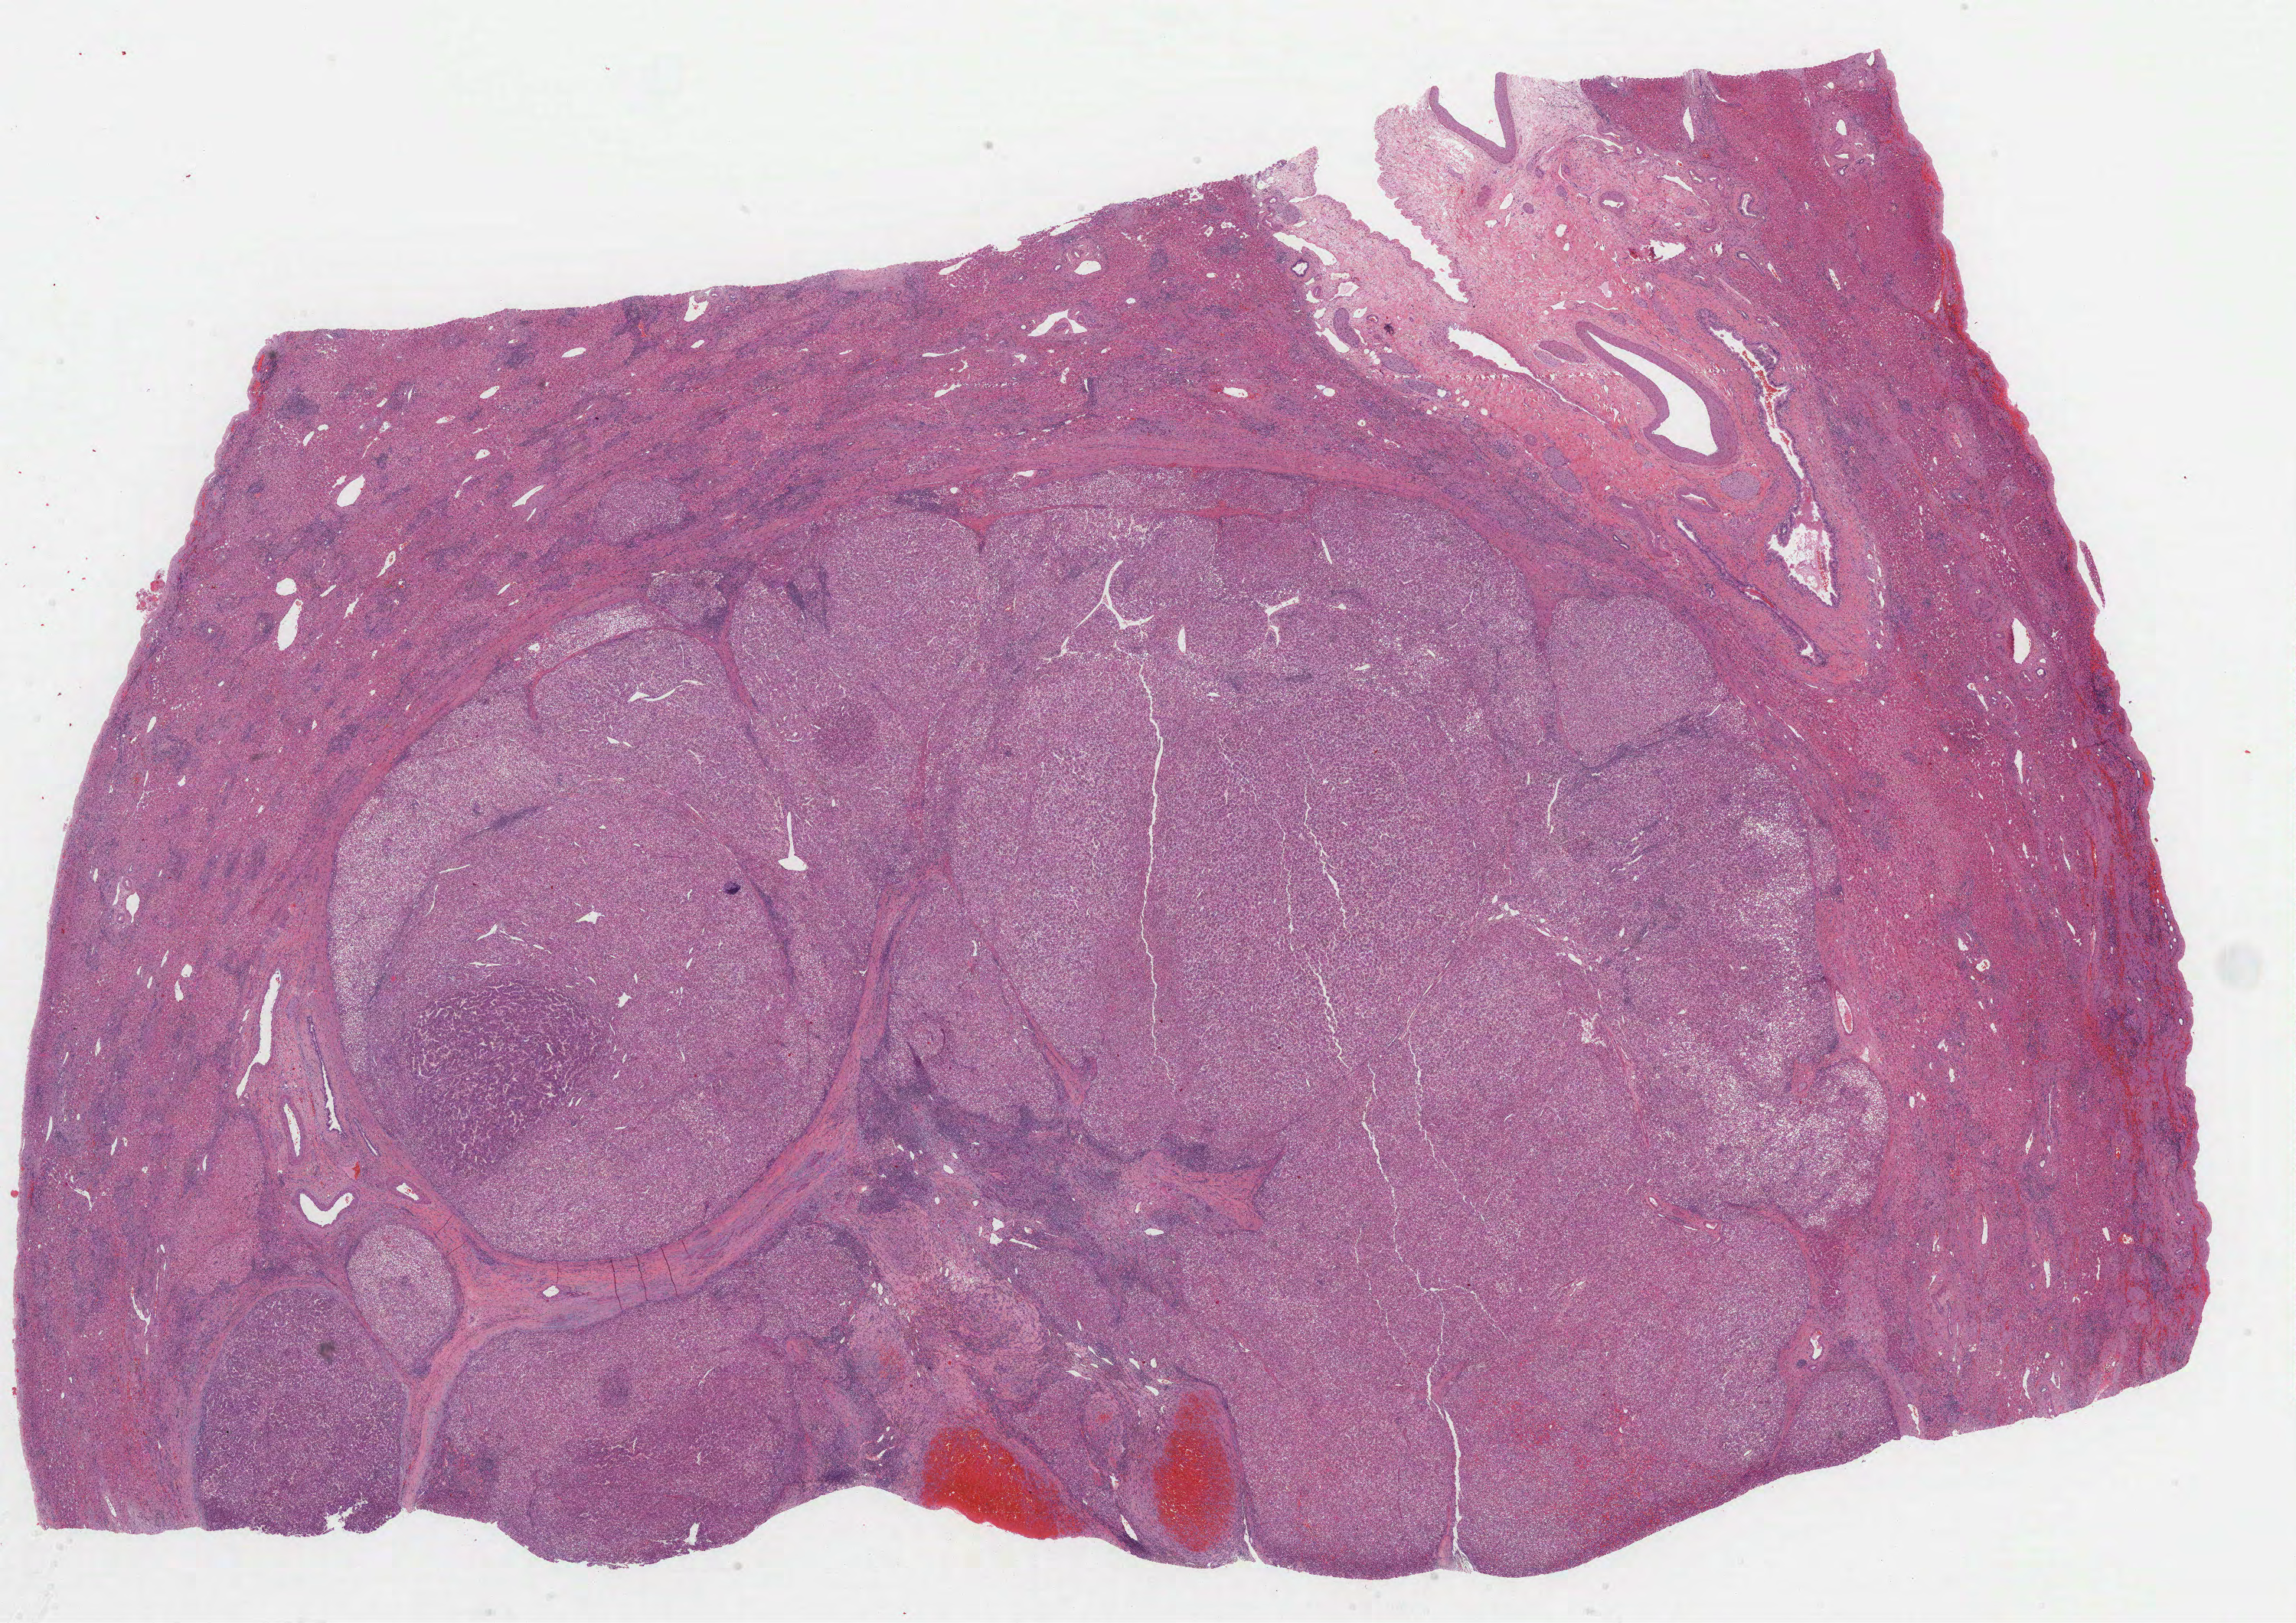
Digitized Hematoxylin and eosin (H&E) stained tissue section (whole slide), a low-resolution overview of the entire scanned area, about 24.2 x 17.1 mm, formalin-fixed paraffin-embedded (FFPE) diagnostic section, liver, primary tumour sample. Female, age 81 years at initial diagnosis. Histologic grade: G2 (moderately differentiated).
AJCC pathologic stage: I (7th edition). Diagnosis: Hepatocellular carcinoma, NOS.